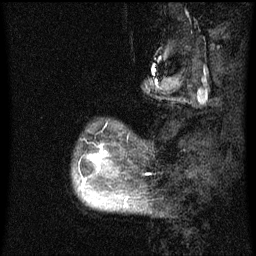
Breast MRI (dynamic contrast-enhanced), one sagittal slice. Slice 11 of 60 in the series (ordered by position). Dynamic contrast-enhanced series, image 2 of 3 at this slice position (ordered by acquisition). 1.5 T. TE 4.2 ms, TR 8 ms. 256 × 256 image matrix, field of view 190 × 190 mm. Patient: female, 50 years.
Outlined on this slice (semi-automatic segmentation, software-assisted and operator-edited):
- analysis volume of interest (the breast-tissue region the enhancement analysis was run in; not a lesion): bounding box [x1, y1, x2, y2] px = [74, 144, 142, 211]
- tumour enhancement mask (voxels above the 70 % enhancement threshold inside the analysis volume of interest): [81, 152, 128, 207]